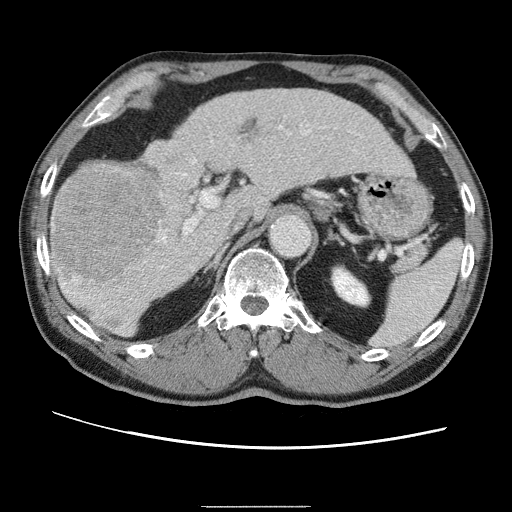
Contrast-enhanced abdominal CT (liver protocol), one axial slice; position 33 of 75 along the scan axis; one of 2 acquisitions stored at this slice position; soft-tissue window (W 400 / L 40 HU); 512 × 512 image matrix, field of view 360 × 360 mm. From the clinical record (not read from this slice): diagnosis: hepatocellular carcinoma (patient treated with transarterial chemoembolisation; whether this scan precedes or follows treatment is not stated here); TNM stage (as recorded): Stage-II; Child-Pugh class: A; tumour nodularity: multinodular; tumour size: 2 cm.
Annotated regions visible in this slice (semi-automatically segmented with operator editing):
- liver parenchyma outside the tumour (the mass and vessels are separate outlines, so this box may not span the whole liver): bounding box <52,90,408,334> (left, top, right, bottom; pixels)
- mass: <53,168,164,291>
- liver vessels: <61,126,286,304>